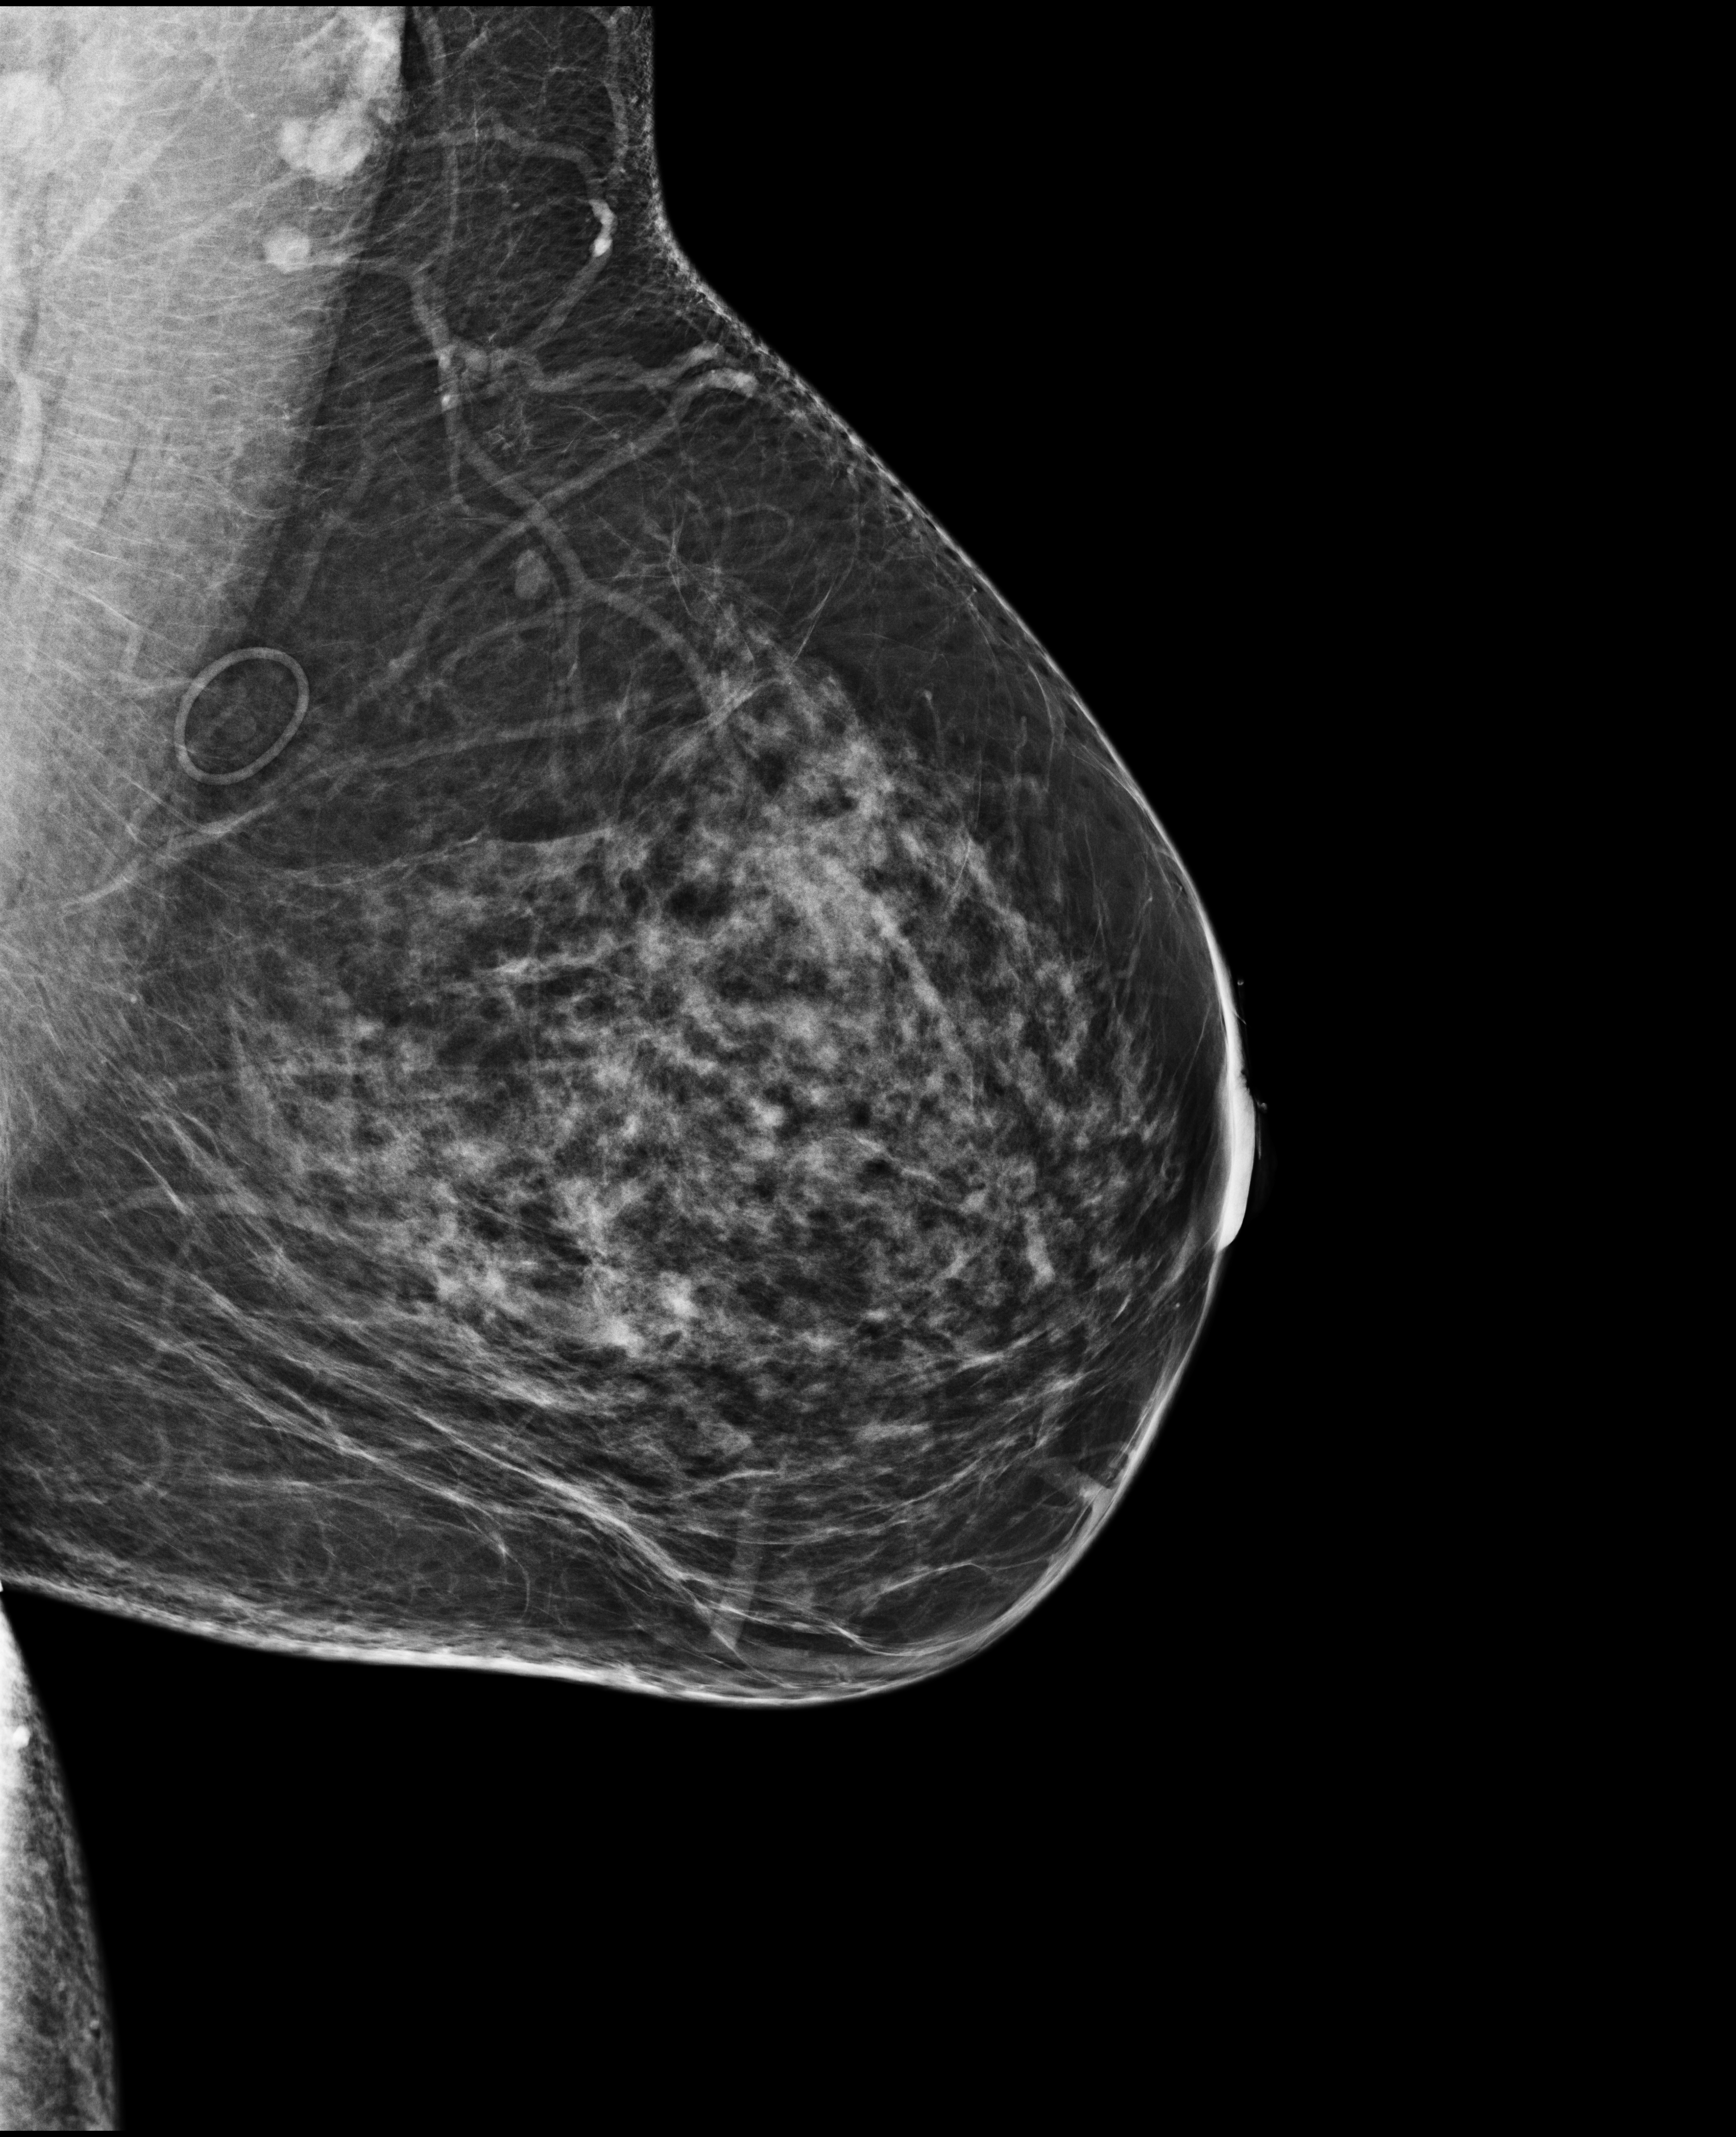
Annual screening mammography examination, compressed breast thickness 78 mm, system: Selenia Dimensions. Patient: female, 51 years.
Image type: full-field digital mammogram. Breast: left. Projection: MLO view.